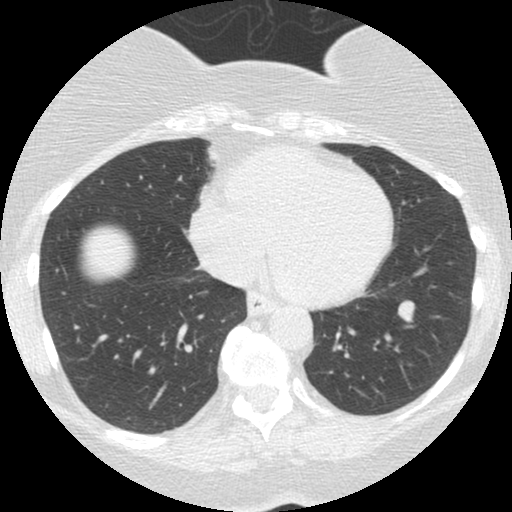
Low-dose screening chest CT, one axial slice. Position 58 of 167 along the scan axis. Reconstruction kernel STANDARD. Lung window (W 1500 / L -600 HU). 2.5 mm slice thickness. 512 × 512 image matrix, field of view 300 × 300 mm.
Structures marked on this image (outlined manually by an expert reader):
- lesion 1 (tumor, lower lobe of left lung): box from (x=398, y=301) to (x=414, y=322) px